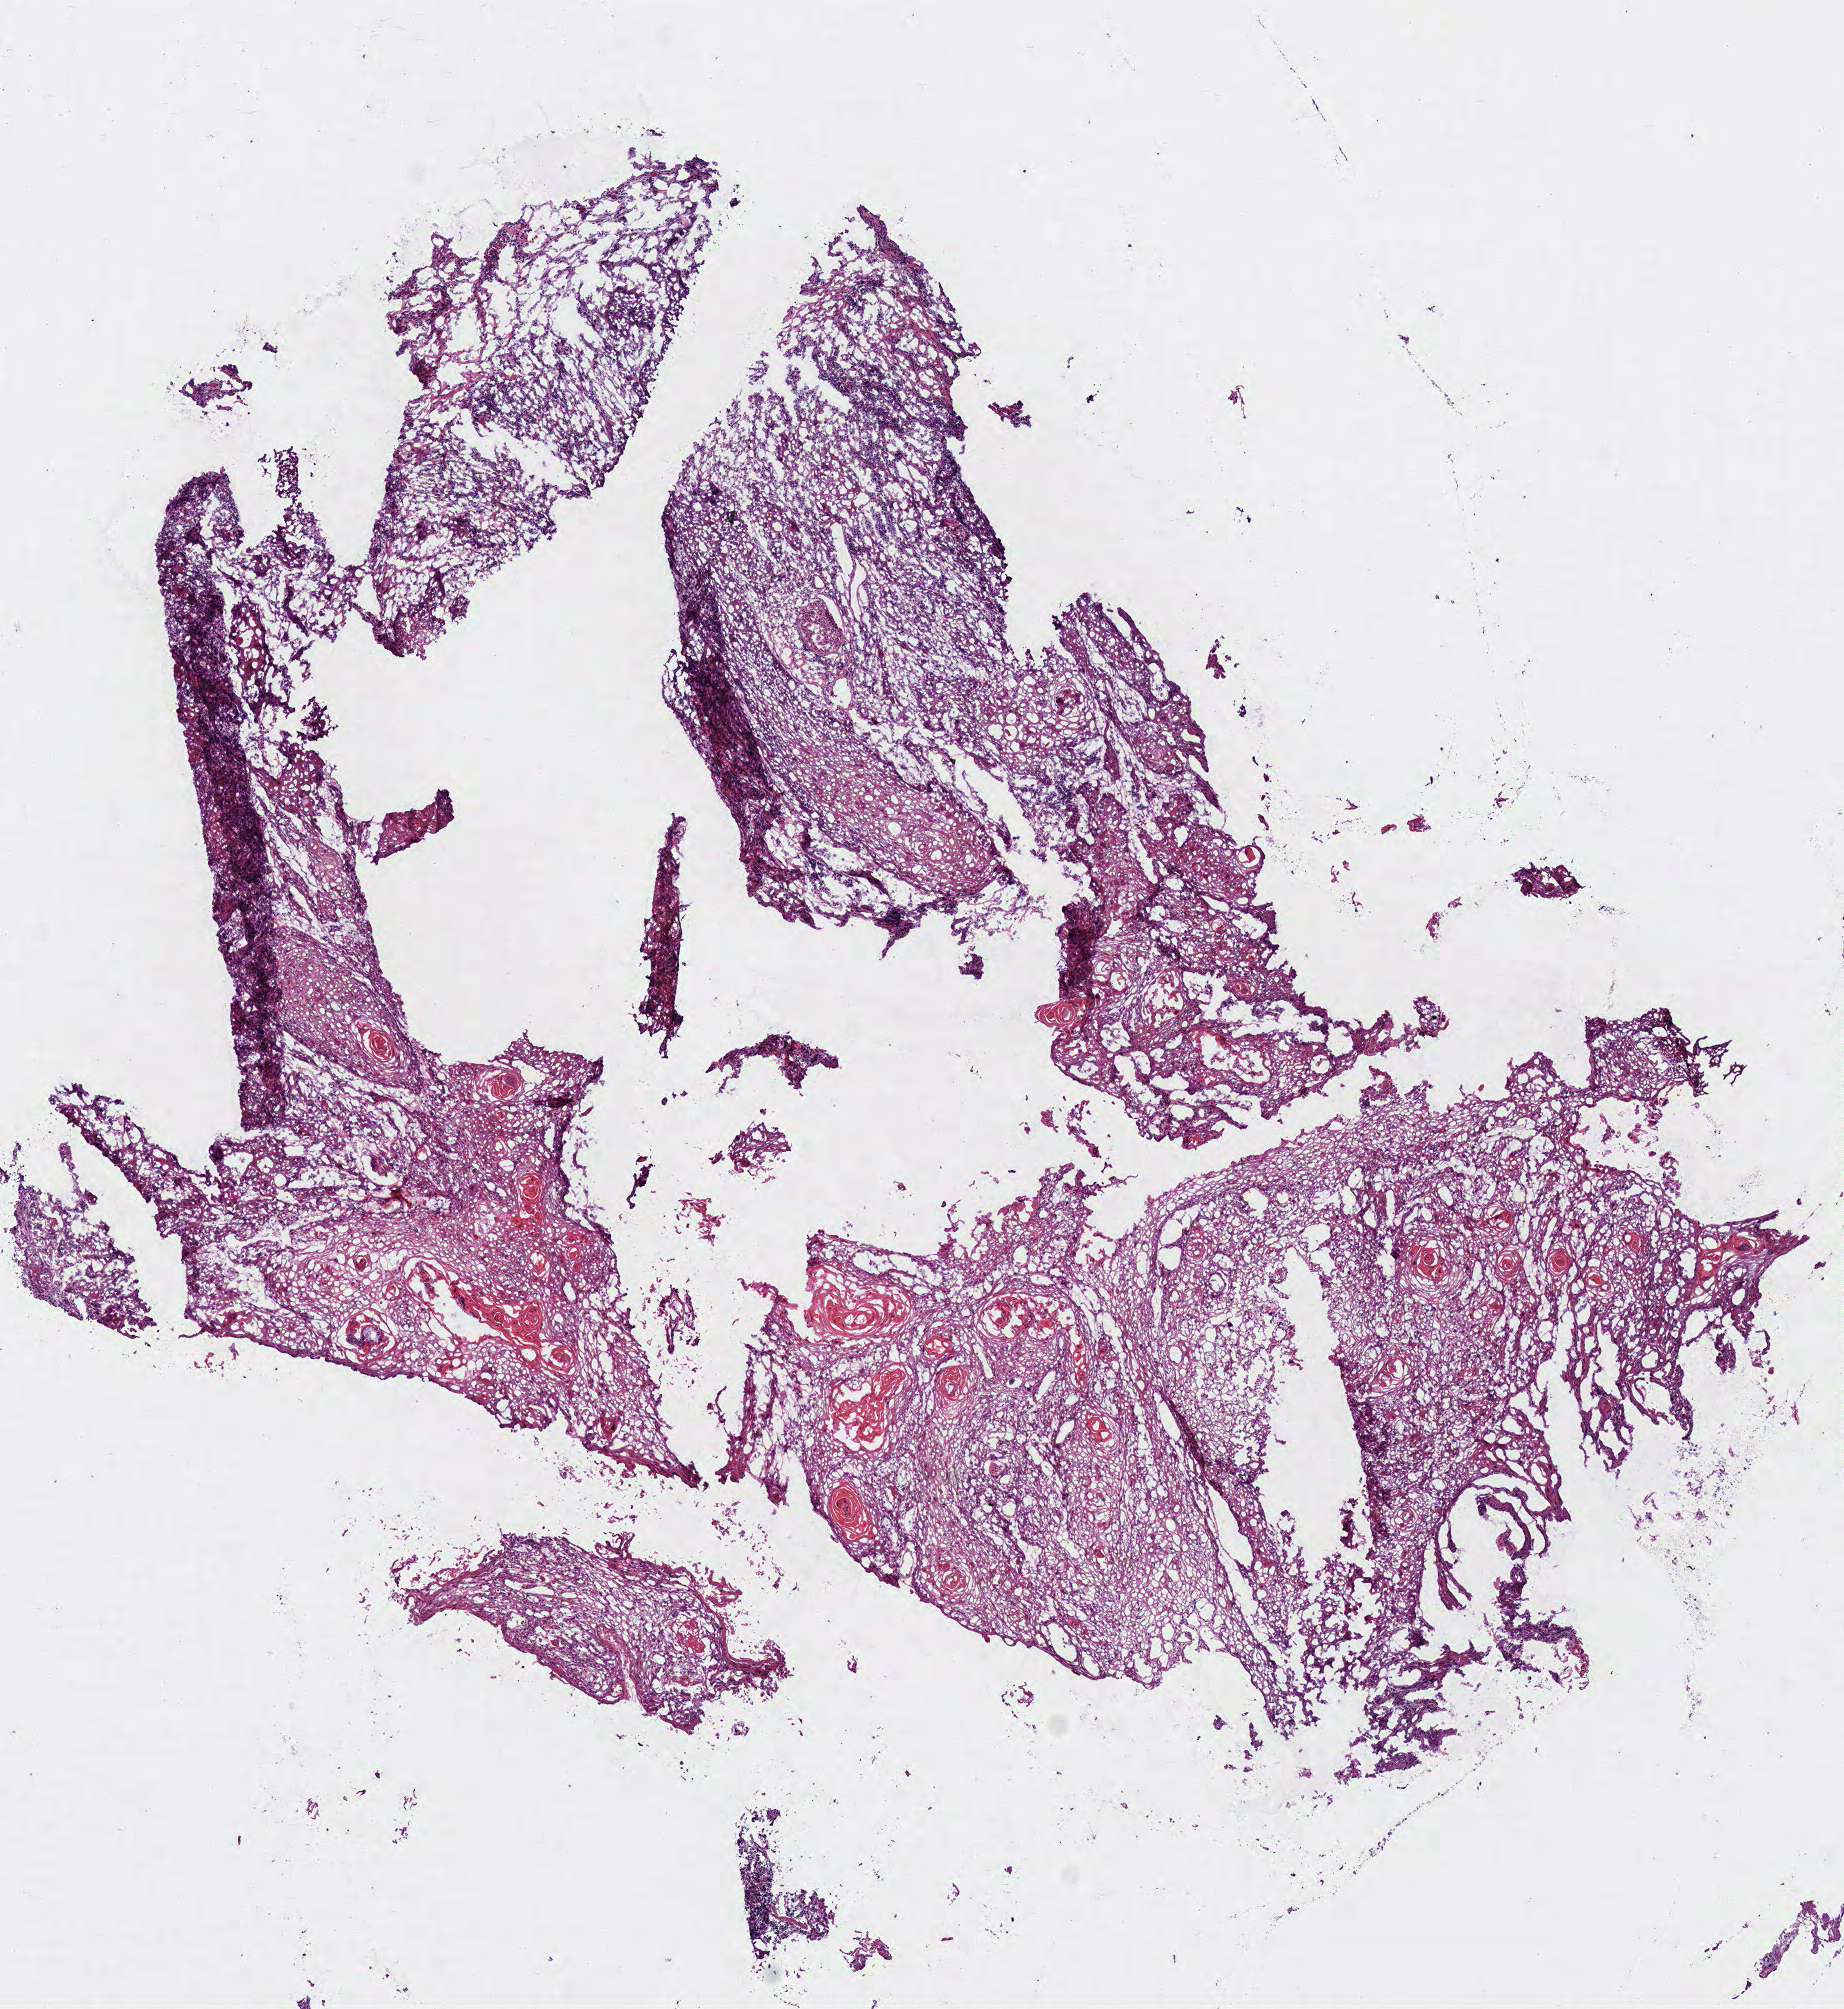
Digitized Hematoxylin and eosin (H&E) stained tissue section (whole slide), a low-resolution overview of the entire scanned area, about 7.3 x 7.9 mm (from a 40x scan); frozen section from the bottom of the tissue portion; head and neck, primary tumour sample. Female, age 62 years at initial diagnosis. Histologic grade: G3 (poorly differentiated). Pathologist review of this section (percent, as recorded): tumour cells 95%, tumour nuclei 85%, normal cells 0%, stromal cells 5%, necrosis 0%.
Diagnosis: Squamous cell carcinoma, NOS (tongue, NOS). AJCC pathologic stage: III (7th edition). TNM: T3 N1.